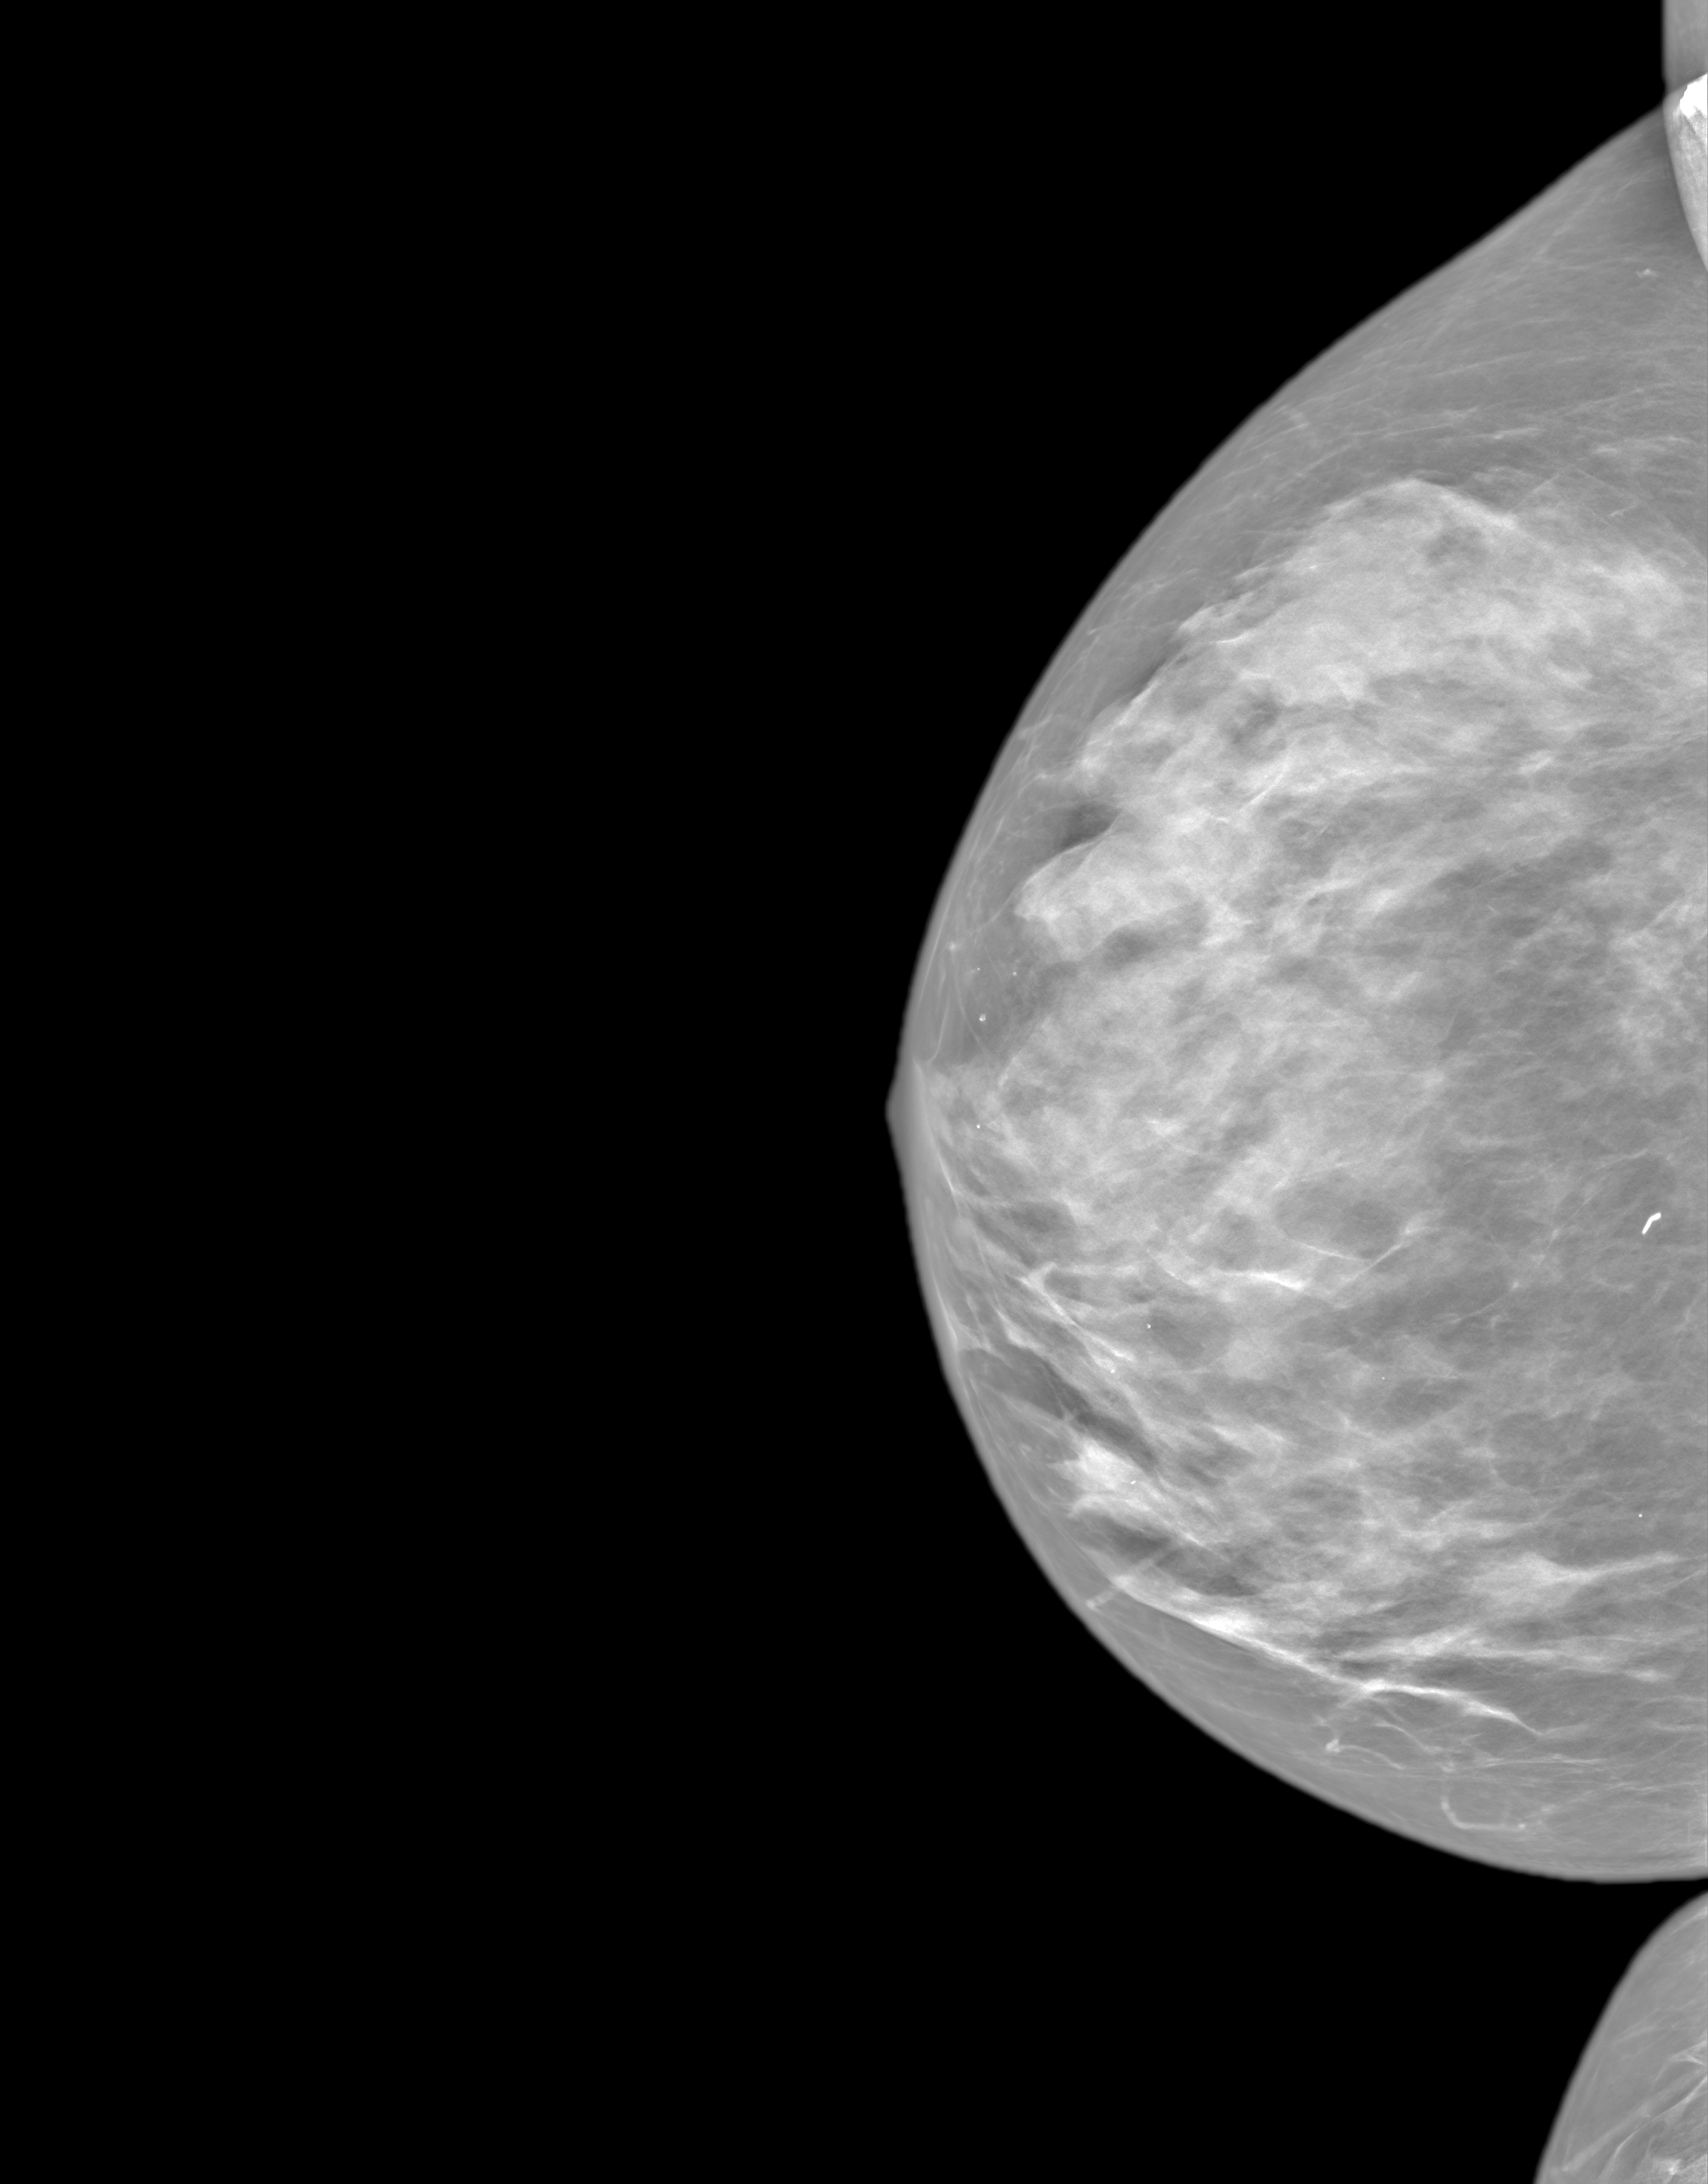
Synthetic 2-D view generated from a tomosynthesis acquisition (not an FFDM exposure); right breast; cranio-caudal projection; annual screening mammography examination; system: SenoIris_1SP1.1(421). Female patient, age 64 years.
BI-RADS breast density category at the screening exam (both breasts, scale 1–4): 4. Final BI-RADS assessment for this screening round (tomosynthesis exam, both breasts): category 2. Recall: no recall after this screen.